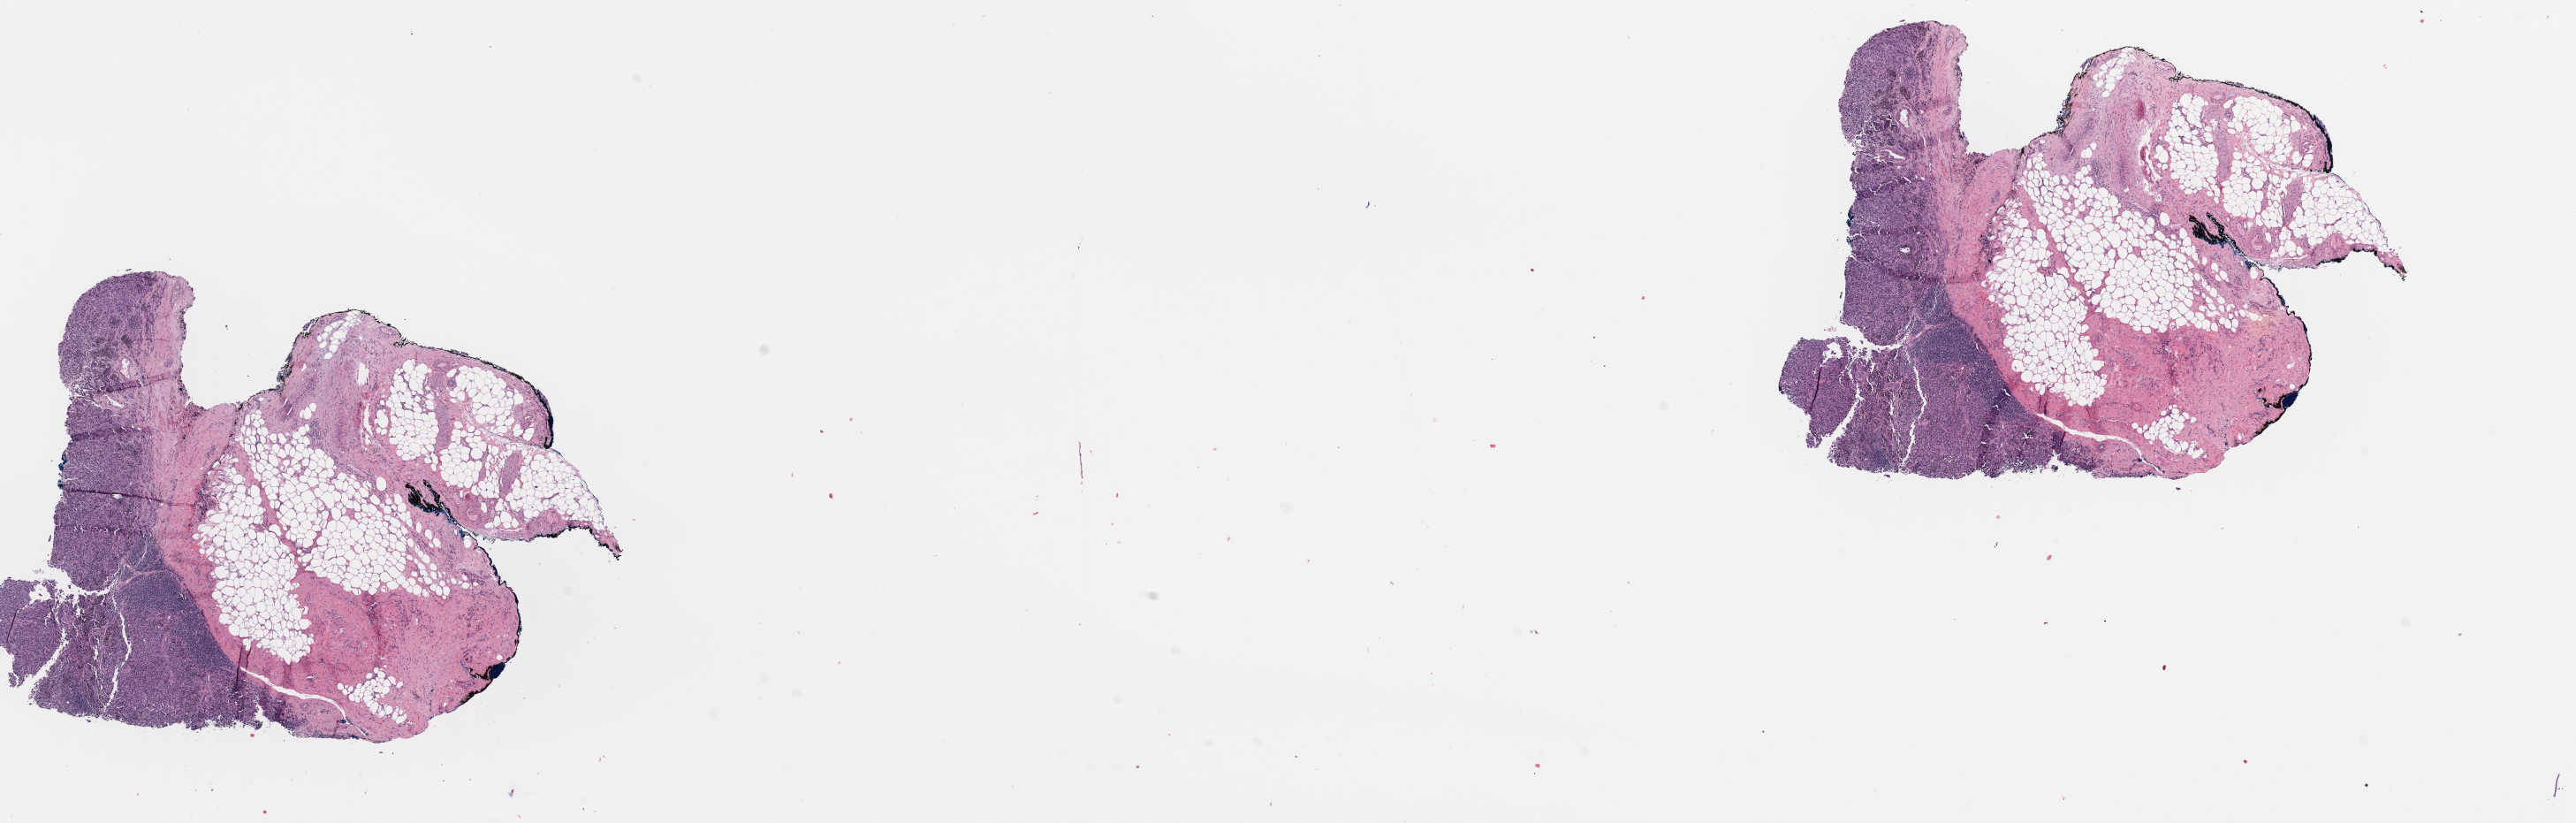
Hematoxylin and eosin (H&E) stained whole-slide image, whole scanned area (about 22.9 x 7.3 mm, slide scanned at 40x) shown as a low-resolution overview. FFPE section. Sample: primary tumour, retroperitoneum and peritoneum. Female, age 46 years at initial diagnosis.
Diagnosis: Paraganglioma, NOS (retroperitoneum).